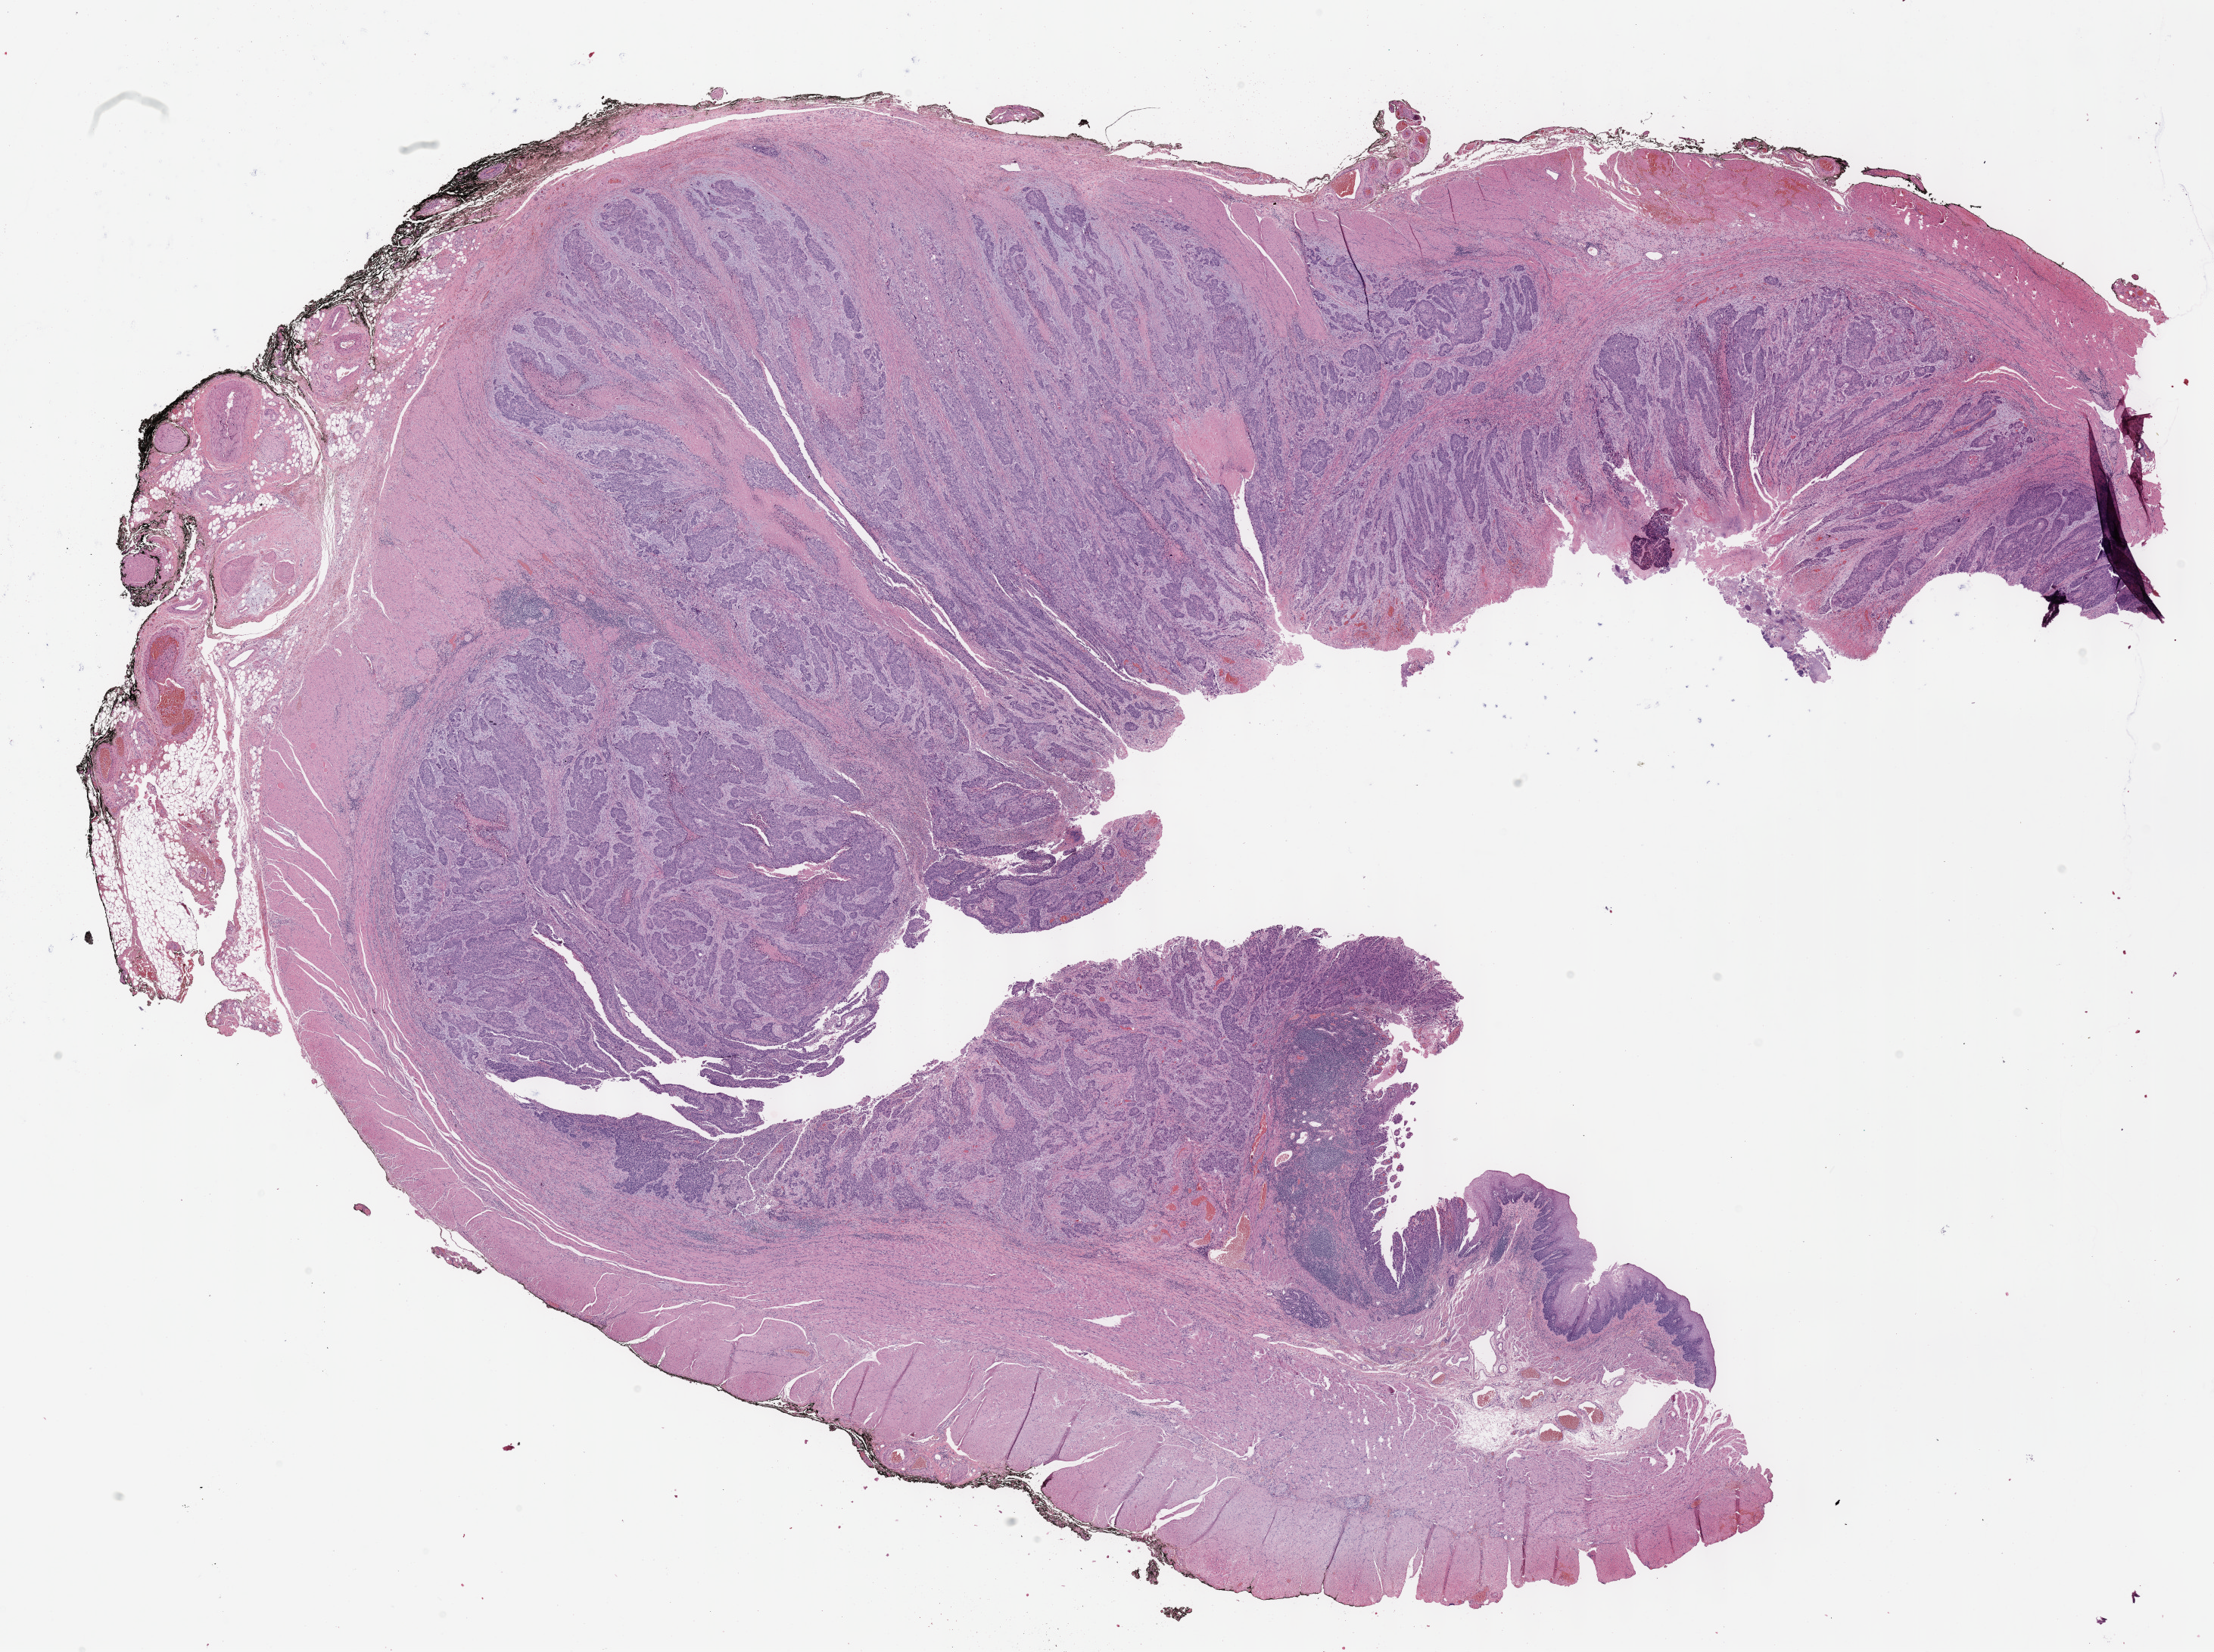
Whole-slide histology image, H&E-stained, a low-resolution overview of the entire scanned area, about 23.6 x 17.6 mm; formalin-fixed paraffin-embedded (FFPE) diagnostic section; sample: primary tumour, esophagus. Female, age 65 years at initial diagnosis. Histologic grade: G2 (moderately differentiated).
Lymph nodes positive (case pathology): 9 of 27 examined. AJCC pathologic stage: IV. Diagnosis: Squamous cell carcinoma, NOS (middle third of esophagus).